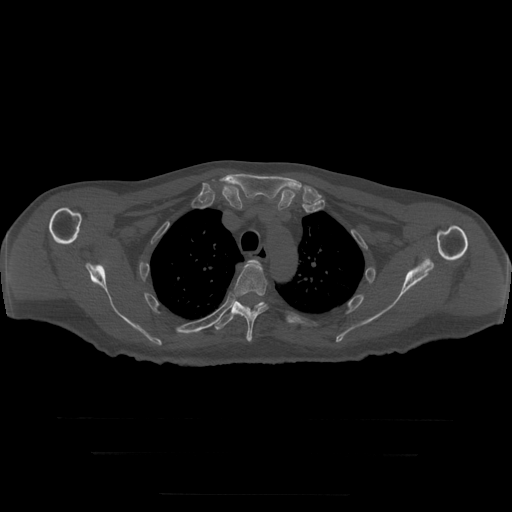
CT including the spine, one axial slice. Slice 238 of 397 in the series (ordered by position). 120 kVp. Bone window (W 1800 / L 400 HU). 1.25 mm slice thickness. 512 × 512 image matrix, field of view 510 × 510 mm. Patient age 73 years. From the clinical record (not read from this slice): primary cancer: prostate.
Outlined on this slice (semi-automatic segmentation, software-assisted and operator-edited):
- T3 vertebra: bounding box (x1, y1, x2, y2) in pixels: (248, 260, 260, 265)
- T4 vertebra: (234, 262, 268, 342)
- T5 vertebra: (215, 300, 265, 330)